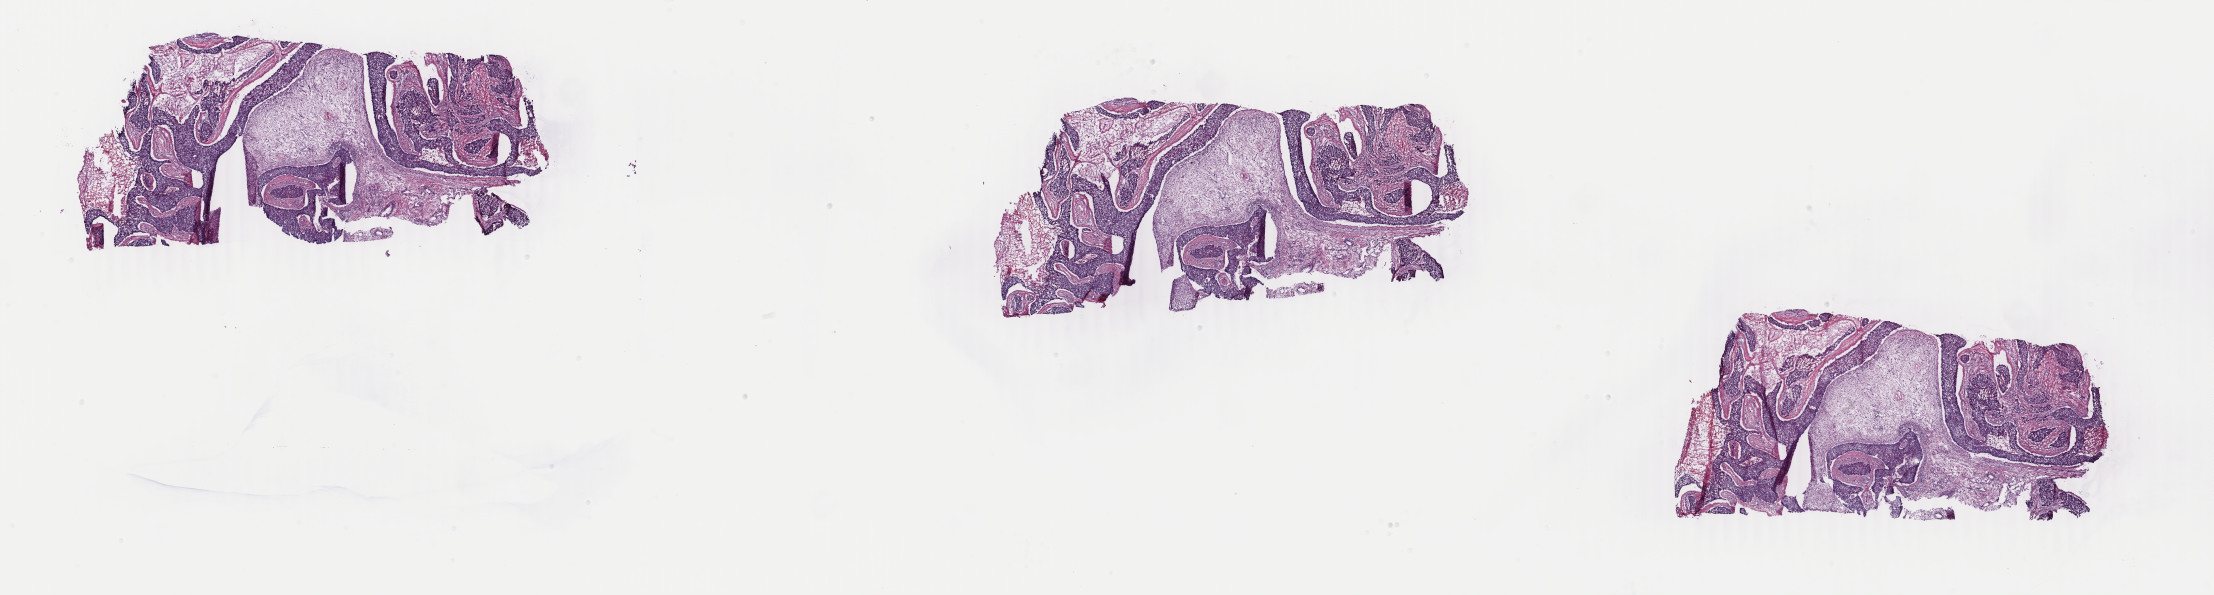
H&E whole-slide image — whole scanned area (about 35.2 x 9.5 mm, acquisition: 40x scan) shown as a low-resolution overview; frozen section from the bottom of the tissue portion; breast, primary tumour sample. Female patient; age at initial diagnosis 59 years. Composition of this section per pathologist review: tumour cells 70%, tumour nuclei 75%, normal cells 0%, stromal cells 21%, necrosis 9%. Inflammatory infiltration, as recorded: lymphocyte infiltration 3%, monocyte infiltration 0%, neutrophil infiltration 0%.
* AJCC pathologic stage: IV
* TNM: T2 N2 M1
* histologic diagnosis: Infiltrating duct carcinoma, NOS